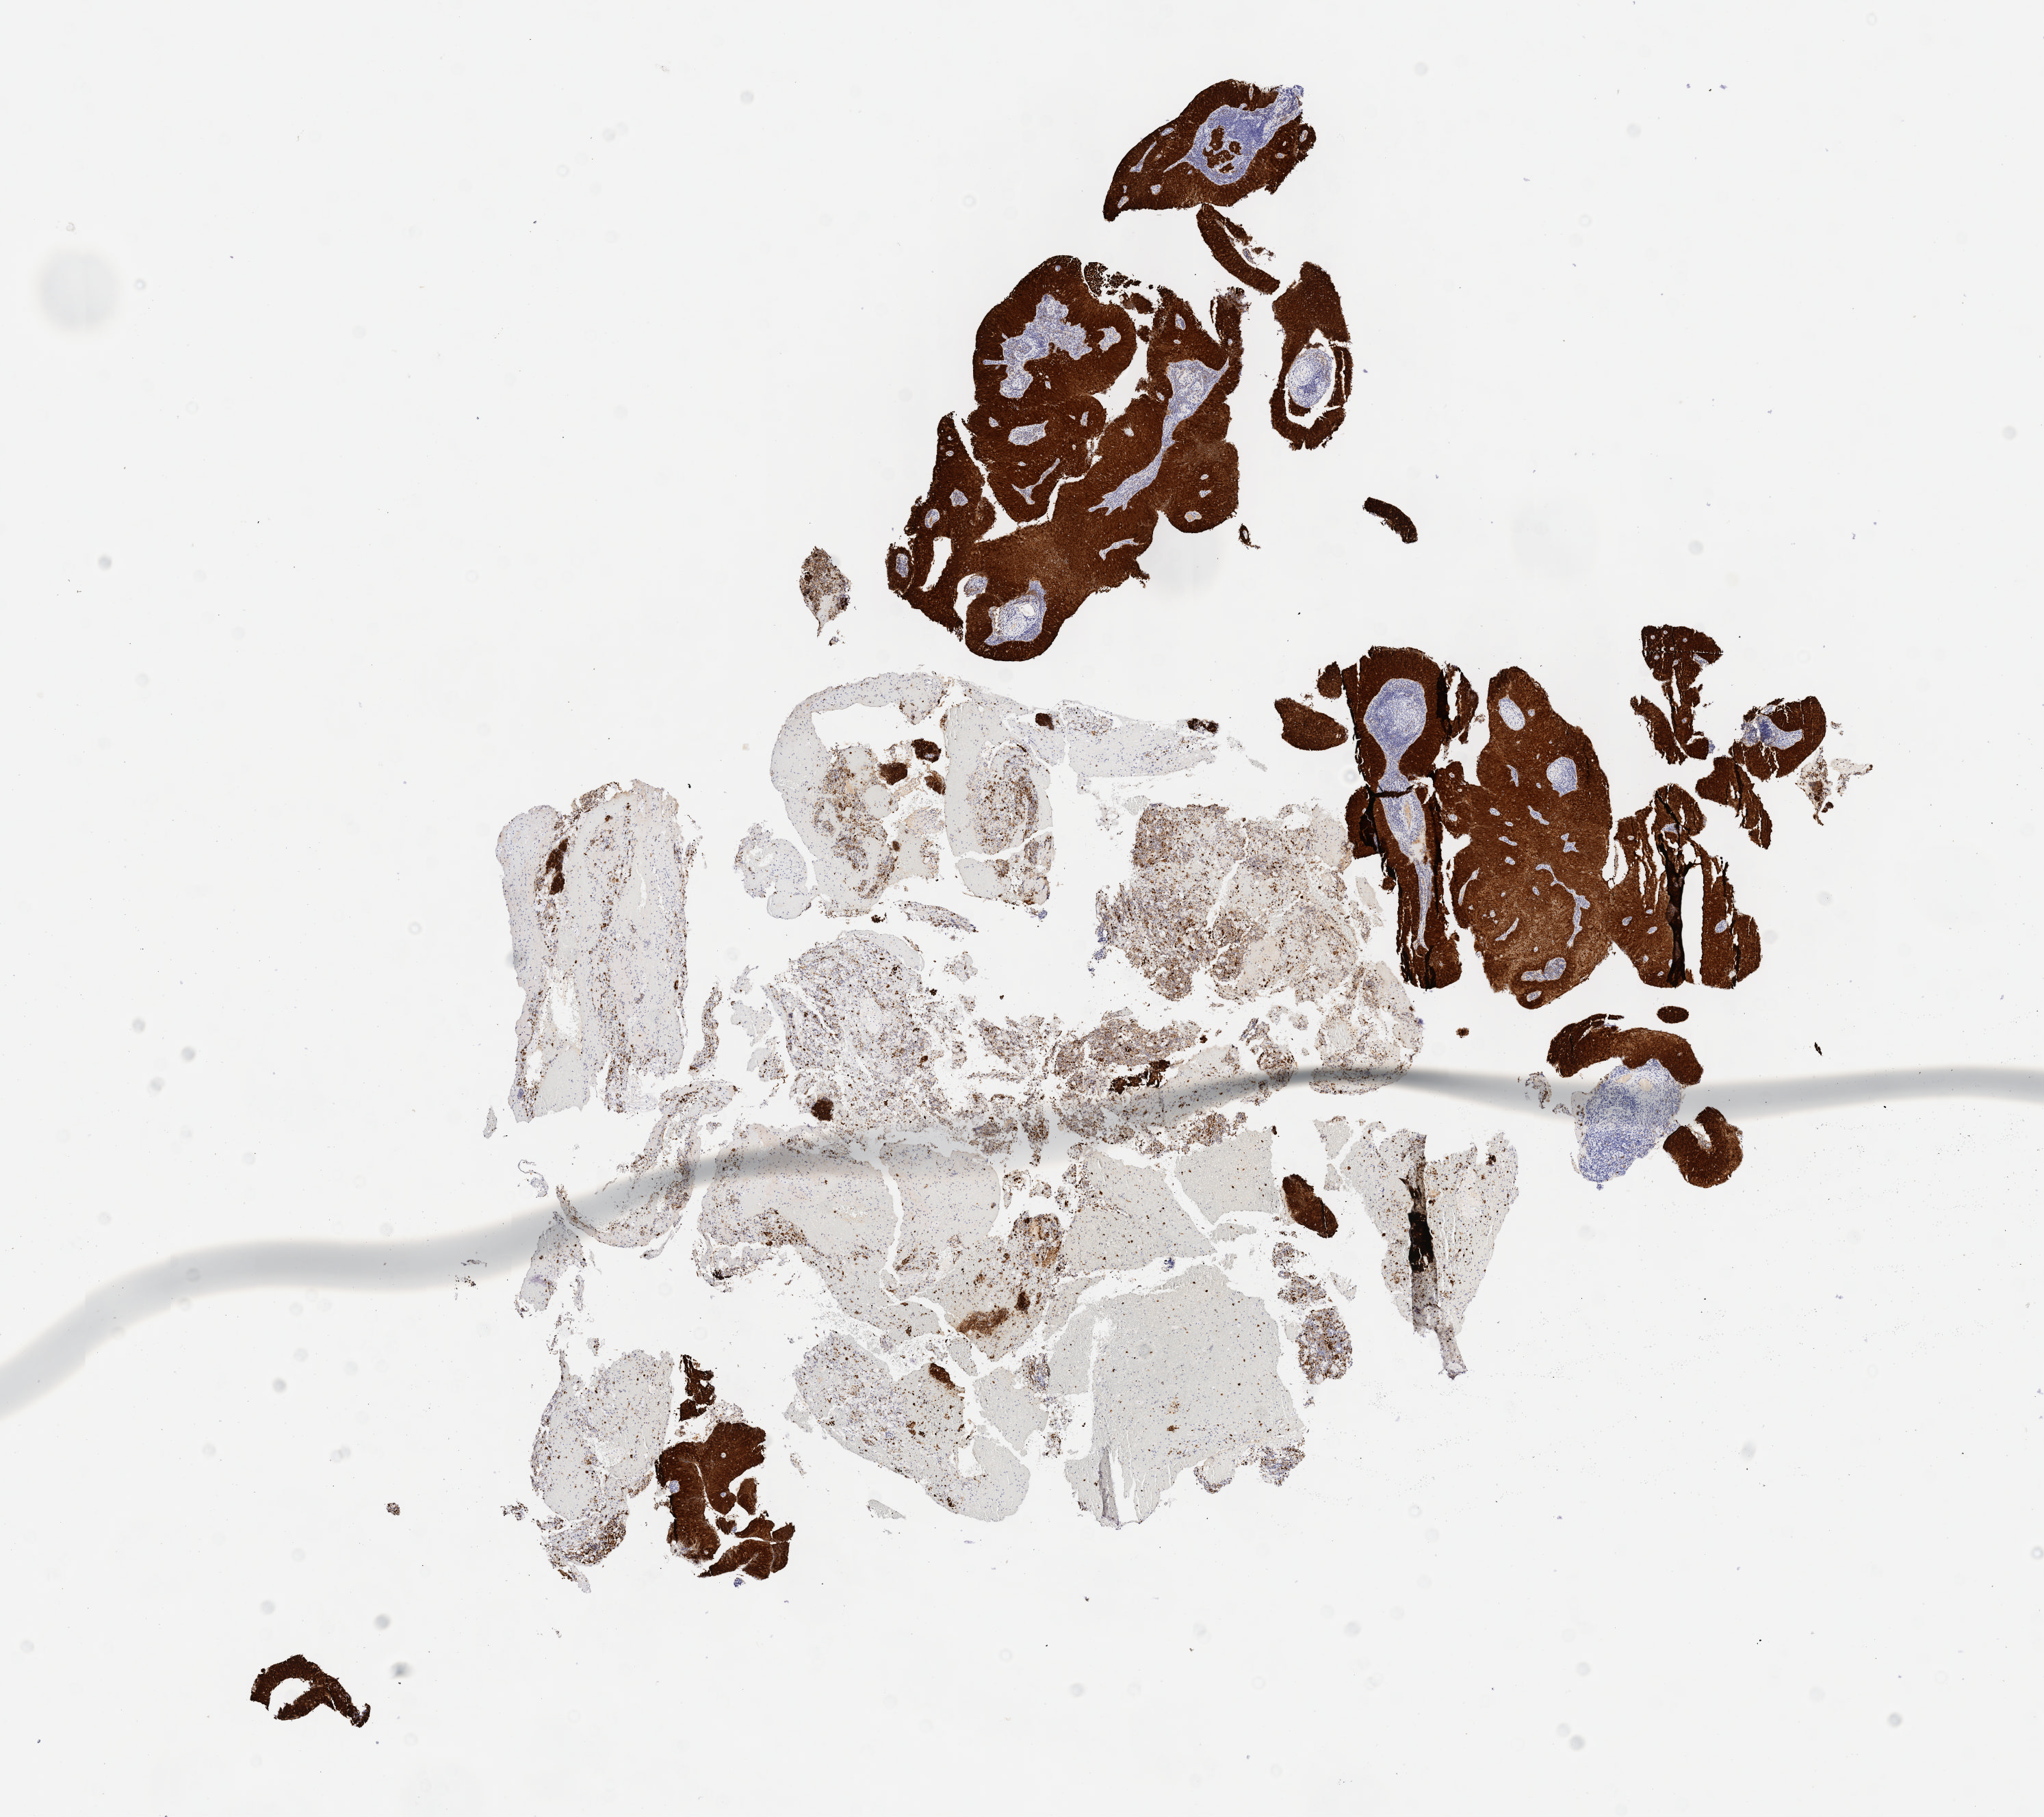
Whole-slide image, immunohistochemical stain for p16 (p16INK4a) — a low-resolution overview of the entire scanned area, about 12.1 x 10.7 mm; tumor tissue; anatomic site: cervix. Female patient, 33 years old.
Diagnosis: Squamous cell carcinoma, large cell, nonkeratinizing, NOS.